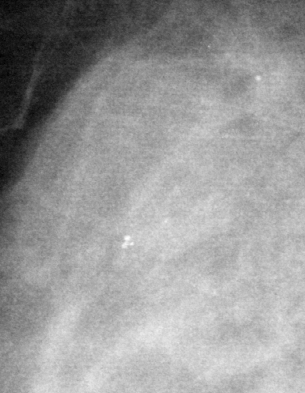
Region of interest cut from a scanned film mammogram (one marked finding); right breast; MLO view; BI-RADS breast density category 3 (scale 1–4).
Finding: calcifications, morphology amorphous, distribution clustered; BI-RADS assessment category 4; pathology result (as recorded, not read from the image): malignant.